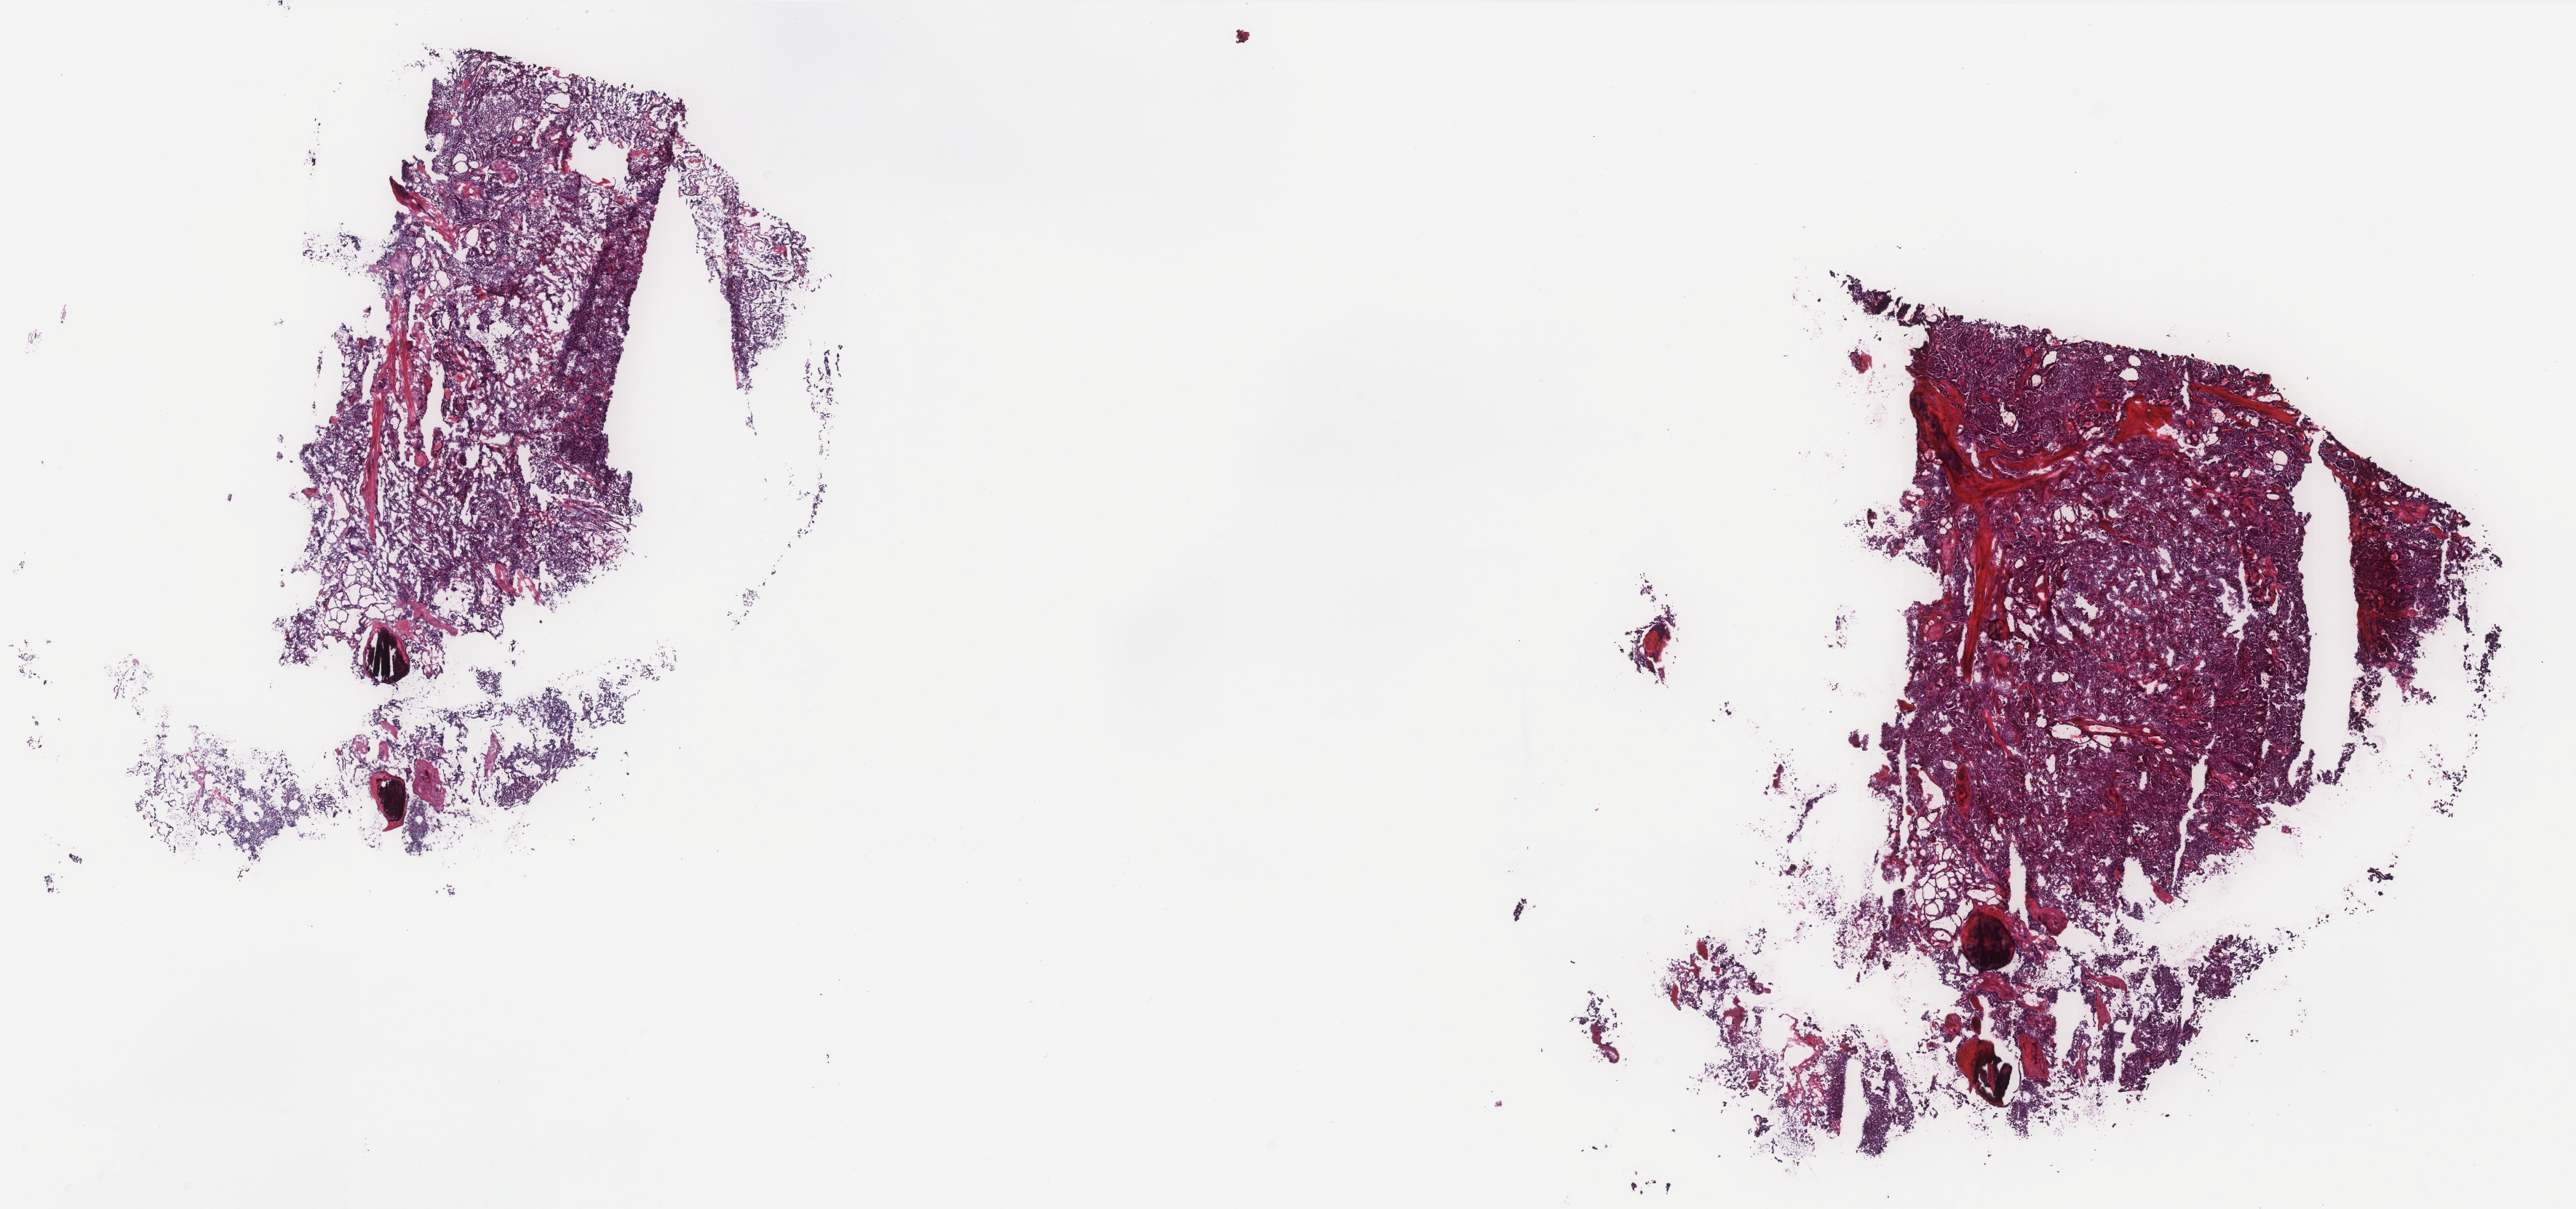
H&E whole-slide image, shown as a low-resolution overview of the whole scanned area (about 28.4 x 13.3 mm, from a 40x scan). Frozen section from the bottom of the tissue portion. Sample: primary tumour, thyroid. Female patient; age at initial diagnosis 52 years. Slide review estimates, as recorded: tumour cells 95%, tumour nuclei 99%, normal cells 0%, stromal cells 5%, necrosis 0%. Infiltration values recorded for this section: lymphocyte infiltration 0%, monocyte infiltration 0%, neutrophil infiltration 0%.
• lymph nodes positive (case pathology): 1 of 4 examined
• AJCC pathologic stage: IVA (7th edition)
• laterality: bilateral
• pathologic diagnosis: Papillary carcinoma, columnar cell (thyroid gland)